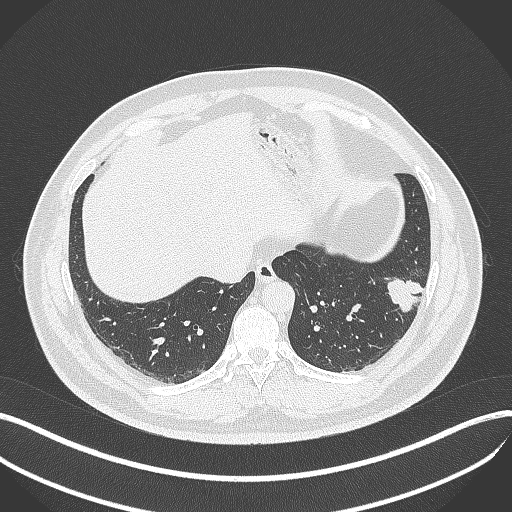
Chest CT, one axial slice. Slice 117 of 429 in the series (ordered by position). Lung window (W 1500 / L -600 HU). 1 mm slice thickness. 512 × 512 image matrix, field of view 400 × 400 mm. Male patient, age 39 years. From the clinical record (not read from this slice): clinical TNM (as recorded): T2a N0 M0.
Structures marked on this image (rectangle marked by the reading radiologist):
- lung tumour (recorded histology: adenocarcinoma): bounding box (x1, y1, x2, y2) in pixels: (383, 270, 426, 314)